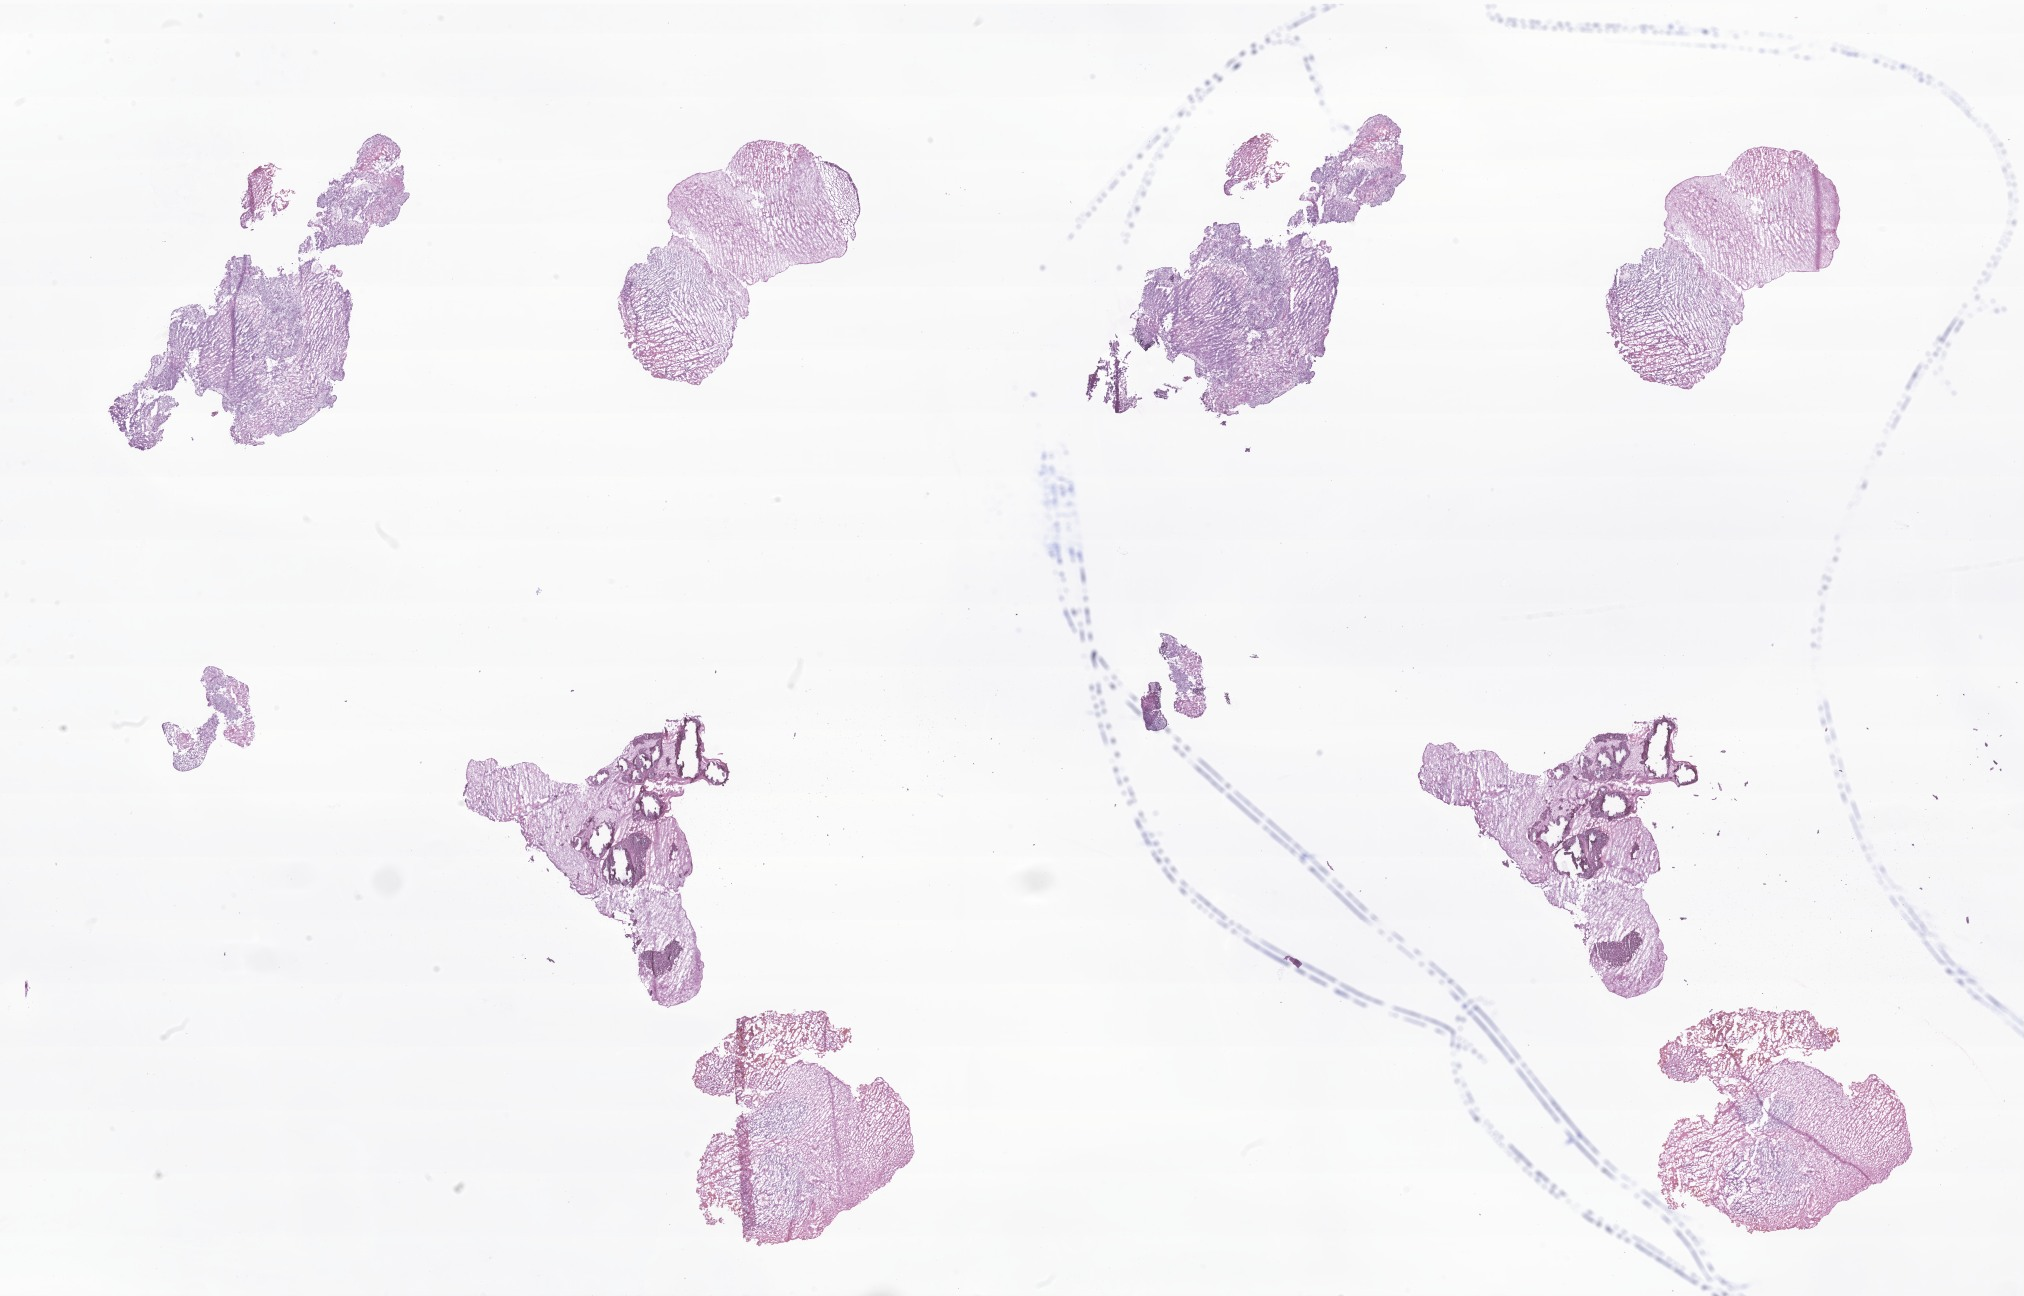
Digitized hematoxylin and eosin (H&E)-stained section of tumor tissue from the brain — a low-resolution overview of the entire scanned area, about 34.1 x 21.9 mm, cryosection (OCT / tissue freezing medium). Male patient, age 79 months.
* diagnosis (ICD-O-3 morphology term): Ependymoma, NOS